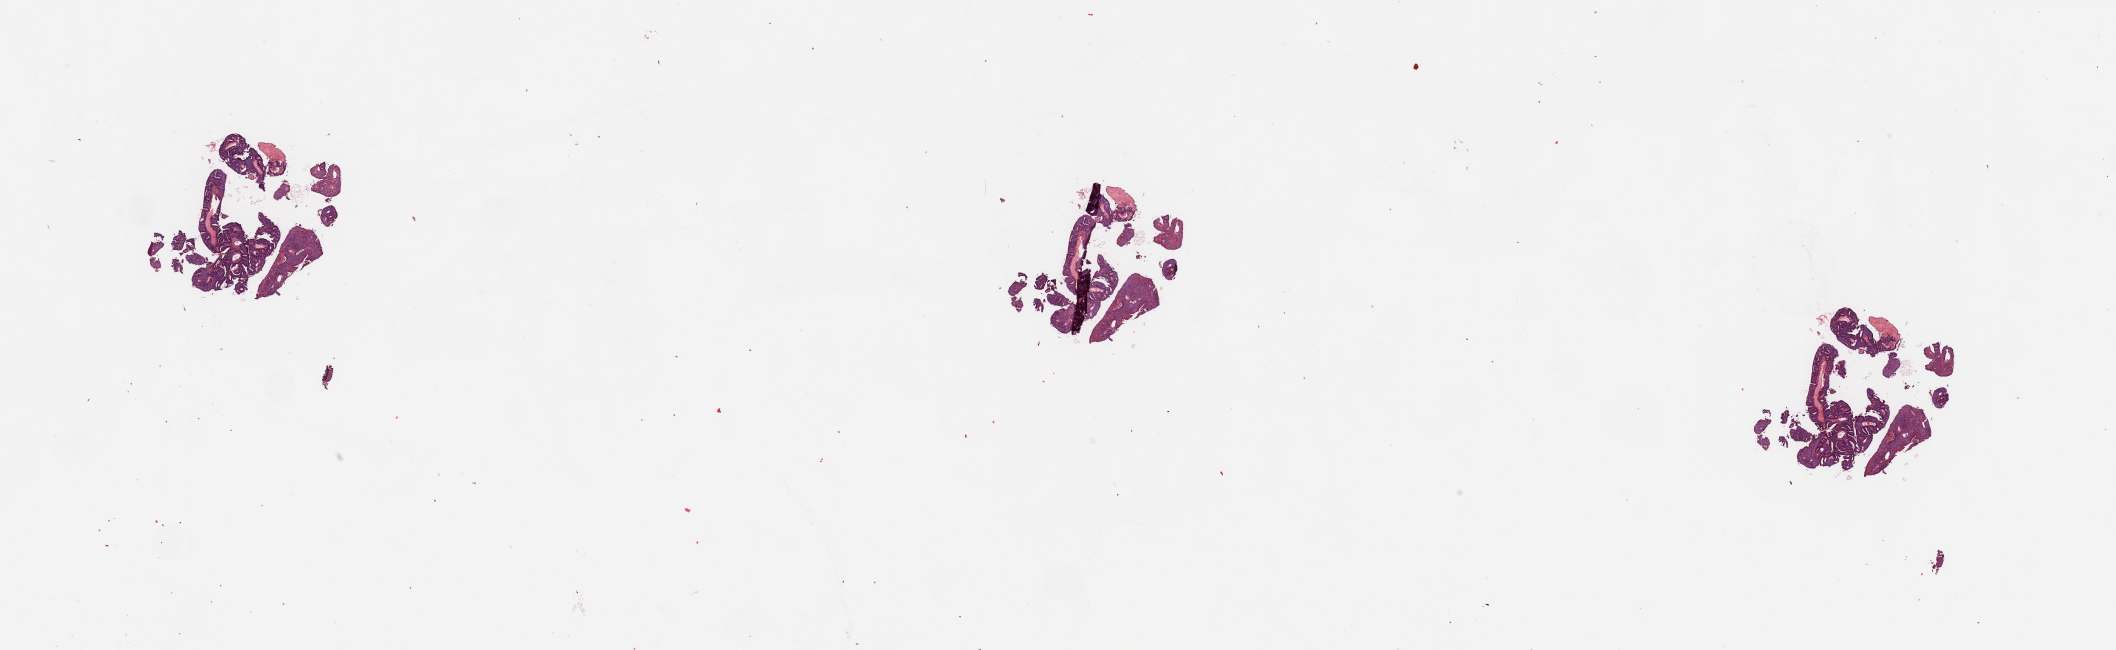
Whole-slide histology image, H&E, a low-resolution overview of the entire scanned area, about 33.5 x 10.3 mm (acquisition: 20x scan); tumour tissue sample, uterus. Patient: female, age 69 years.
Histologic diagnosis: Endometrioid adenocarcinoma, NOS.